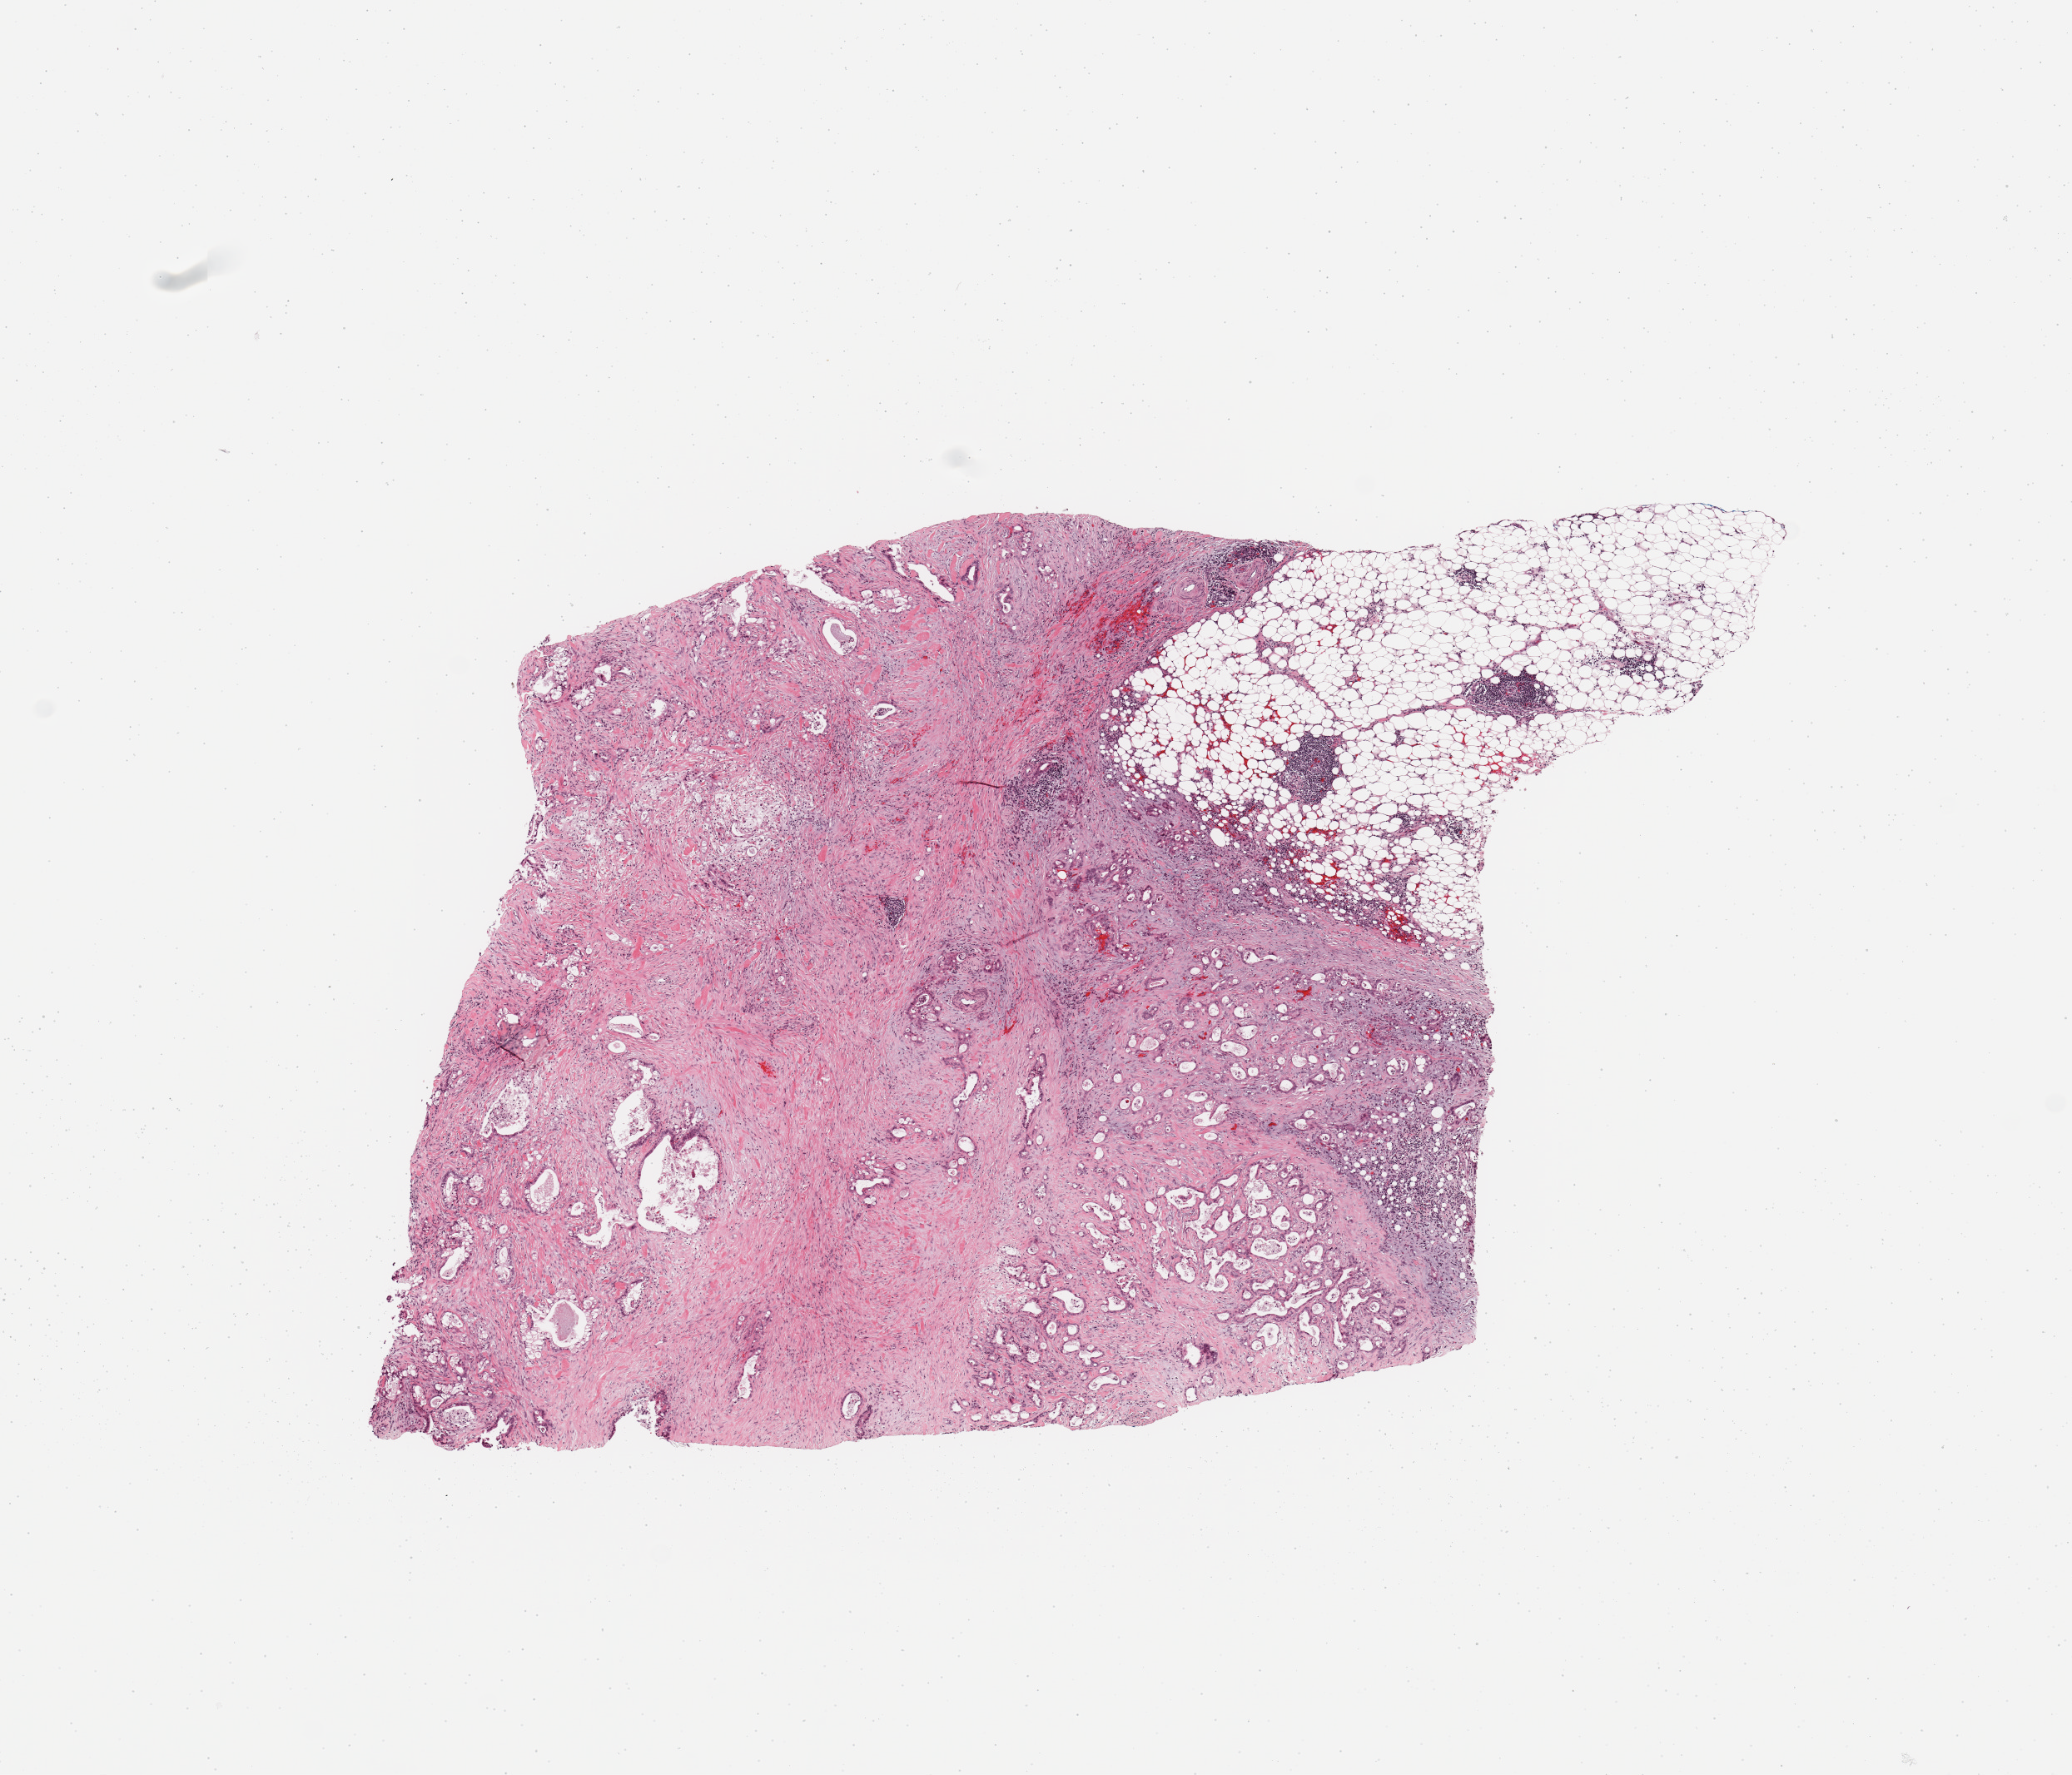
H&E whole-slide image — low-resolution overview of the scanned area, about 9.8 x 8.4 mm (acquisition: 20x scan). Tumour tissue sample, sampled site: pancreas. 58-year-old female patient. Histologic grade: G1 (well differentiated). Pathologist review of this section (percent, as recorded): tumour nuclei 30%, necrosis 0%.
• diagnosis: Infiltrating duct carcinoma, NOS
• AJCC pathologic stage: IIB